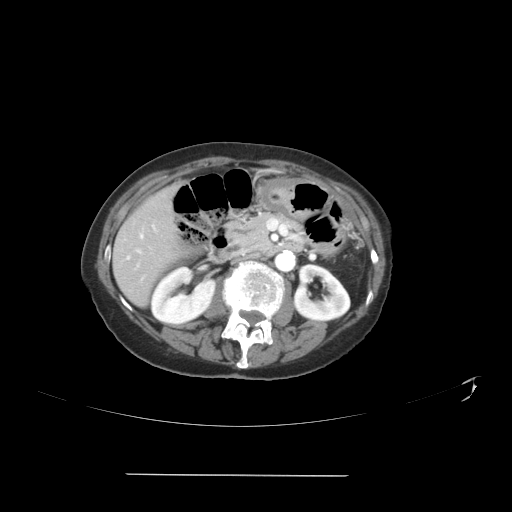
Contrast-enhanced abdominal CT, one axial slice; slice 16 of 41 in the series (ordered by position); intravenous contrast given; soft-tissue window (W 400 / L 40 HU); 5 mm slice thickness; 512 × 512 image matrix, field of view 431 × 431 mm. Female patient, age 74 years. From the clinical record (not read from this slice): diagnosis: colorectal cancer liver metastases, imaged before liver resection; multiple liver metastases: yes; largest metastasis: 3.3 cm; disease in both lobes: yes.
Structures marked on this image (expert manual segmentation):
- hepatic veins: bounding box [x1, y1, x2, y2] px = [127, 234, 144, 259]
- liver: [113, 192, 182, 303]
- planned liver remnant (the part of the liver to remain after resection): [119, 192, 176, 245]
- portal vein (with intrahepatic branches): [137, 250, 140, 252]